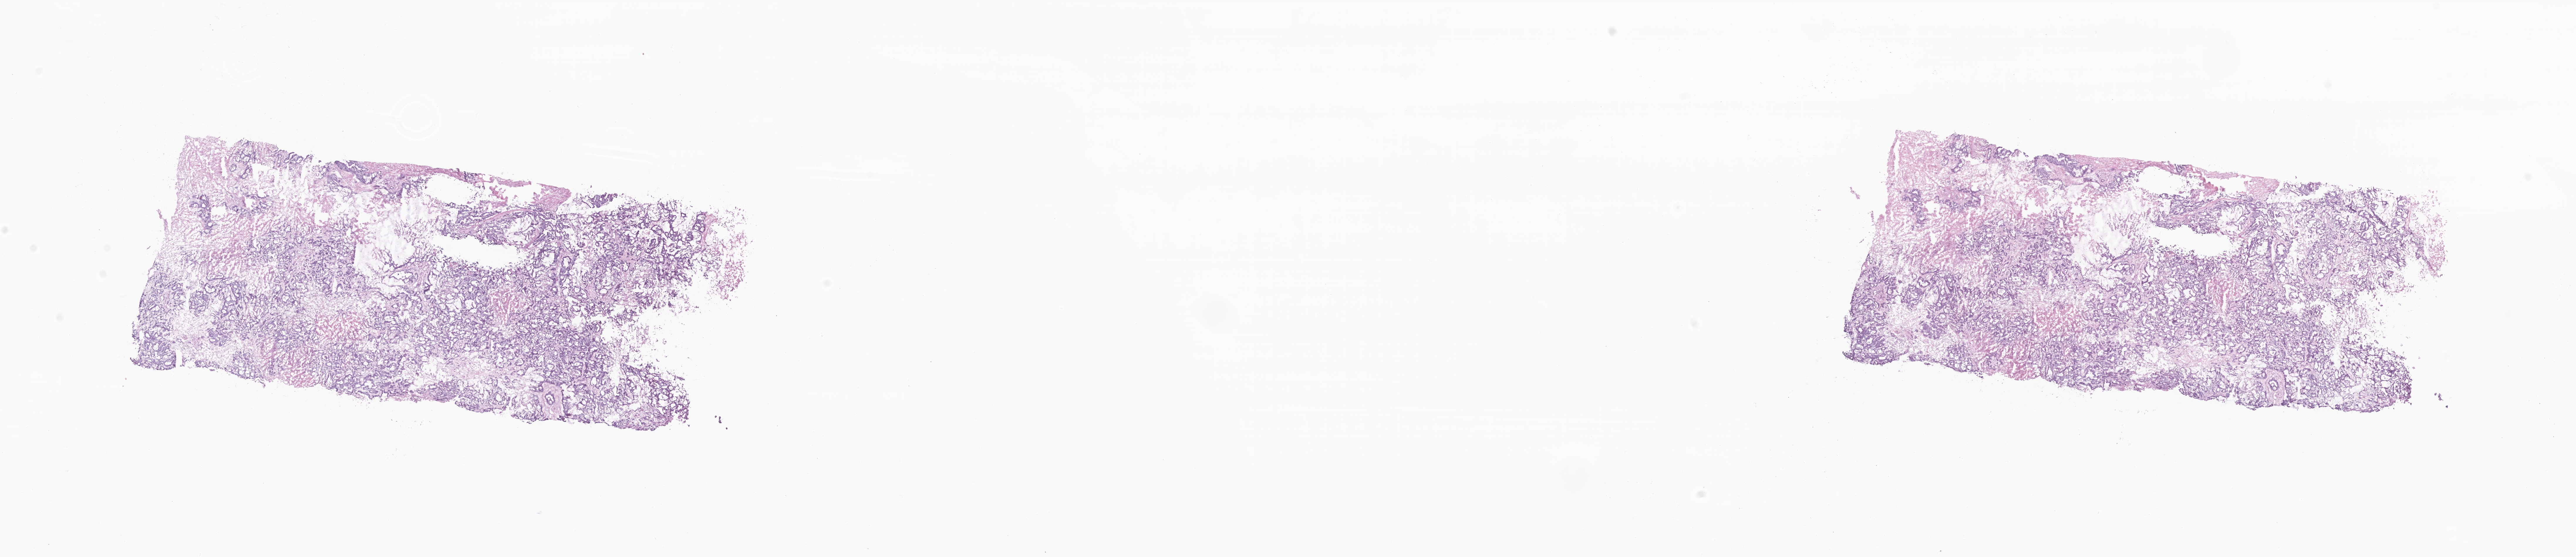
Whole-slide image, H&E stain — whole scanned area (about 37.0 x 8.0 mm) shown as a low-resolution overview, cryosection, specimen: metastatic tumor tissue, resected from liver. Patient: female, age at initial diagnosis 49 years. Pathologist review of this section (percent, as recorded): tumor cells 57%, tumor nuclei 82%, stromal cells 14%, necrosis 17%, normal cells 12%. Infiltration values recorded for this section: lymphocyte infiltration 1%, monocyte infiltration 1%, neutrophil infiltration 0%.
• section: top of the tissue portion
• patient diagnosis (primary): Adenocarcinoma, NOS